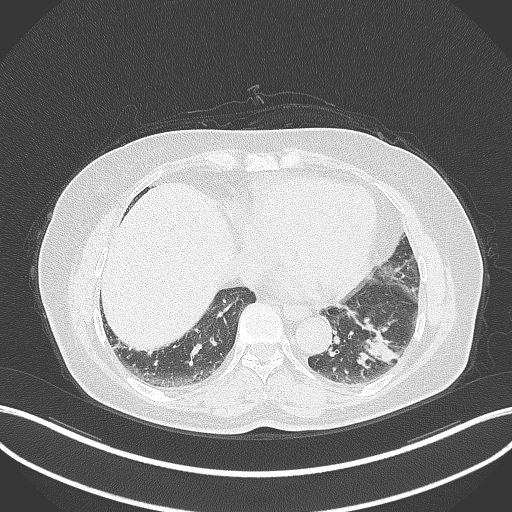
Chest CT, one axial slice. Slice 121 of 311 in the series (ordered by position). Reconstruction kernel B70f. 120 kVp. Lung window (W 1500 / L -600 HU). 1 mm slice thickness. 512 × 512 image matrix. Patient: female, 59 years. From the clinical record (not read from this slice): clinical TNM (as recorded): T2a N0 M0.
Annotated regions visible in this slice (rectangle marked by the reading radiologist):
- lung tumour (recorded histology: adenocarcinoma): bounding box (x1, y1, x2, y2) in pixels: (352, 315, 401, 371)